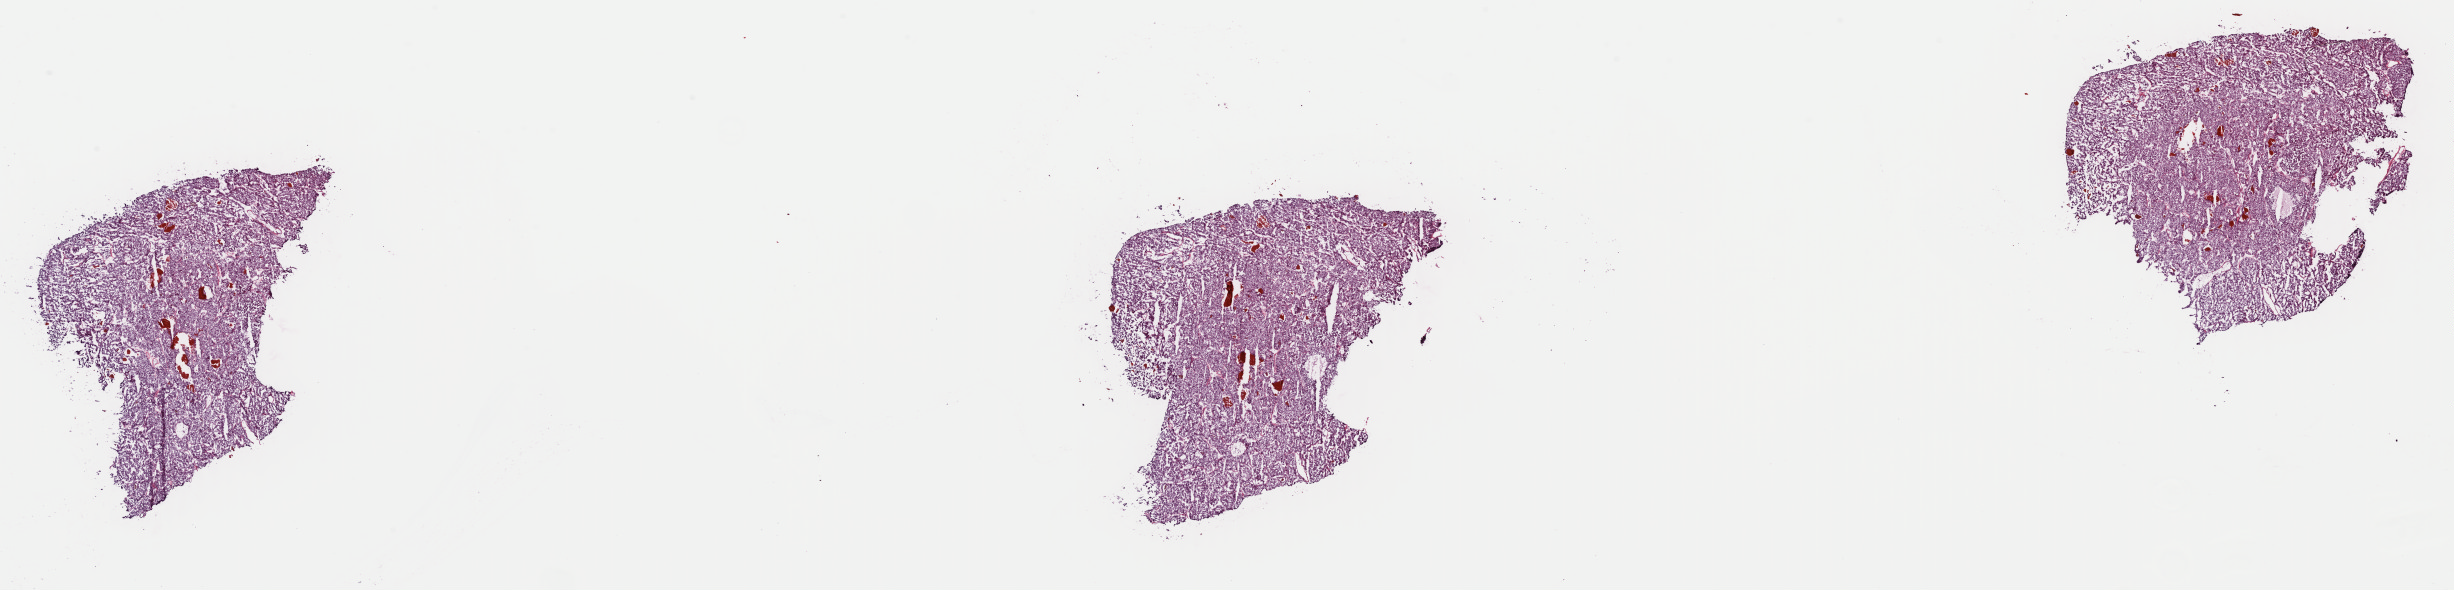
H&E whole-slide image, low-resolution overview of the scanned area, about 38.7 x 9.3 mm (acquisition: 40x scan), frozen section from the top of the tissue portion, primary tumour sample from the kidney. Patient: female, age at initial diagnosis 50 years. Composition of this section per pathologist review: tumour cells 95%, tumour nuclei 95%, normal cells 0%, stromal cells 5%, necrosis 0%. Inflammatory infiltration, as recorded: lymphocyte infiltration 0%, monocyte infiltration 0%, neutrophil infiltration 0%.
- pathologic diagnosis: Renal cell carcinoma, chromophobe type
- AJCC pathologic stage: I (7th edition)
- TNM: T1b NX
- laterality: left